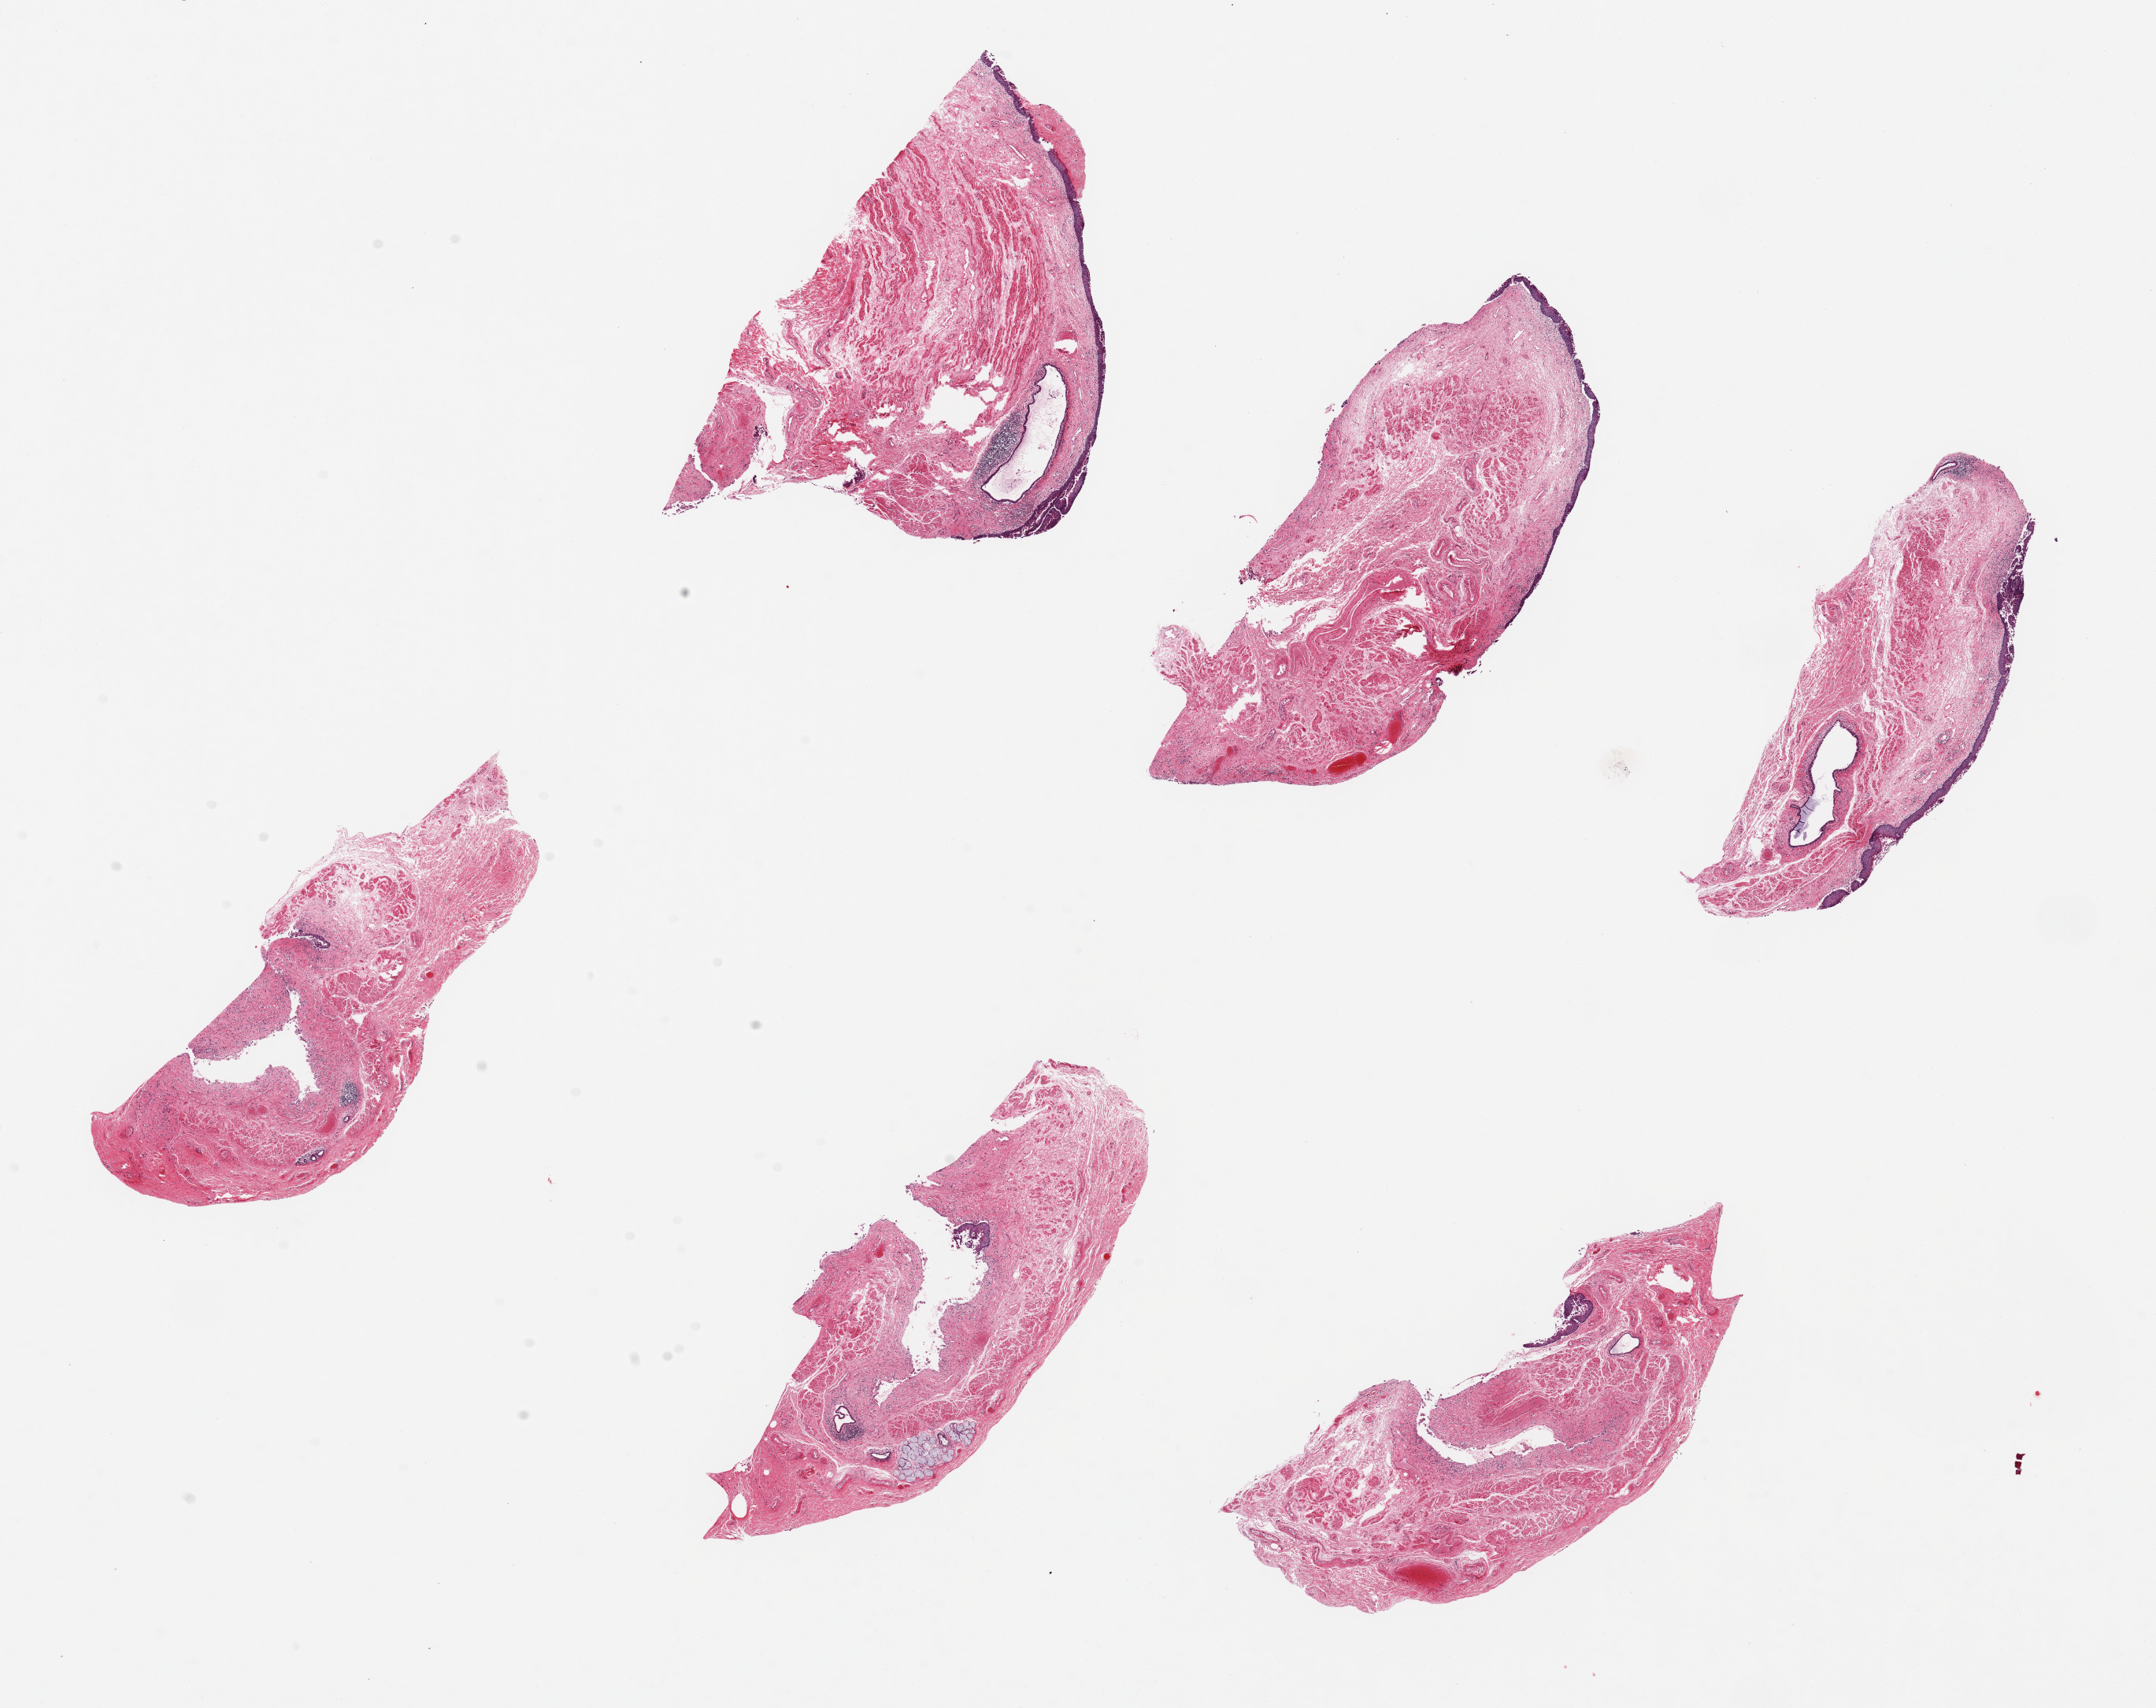
Digitized H&E-stained section, brightfield, a low-resolution overview of the entire scanned area, about 21.7 x 17.2 mm, PAXgene-fixed paraffin-embedded (PFPE) section, sampled site (target tissue): esophageal mucous membrane, donor tissue sample.
* pathologist's review note for this sample: 6 pieces, 5x2mm. Squamous mucosa largely sloughed, 2-3% of thickness